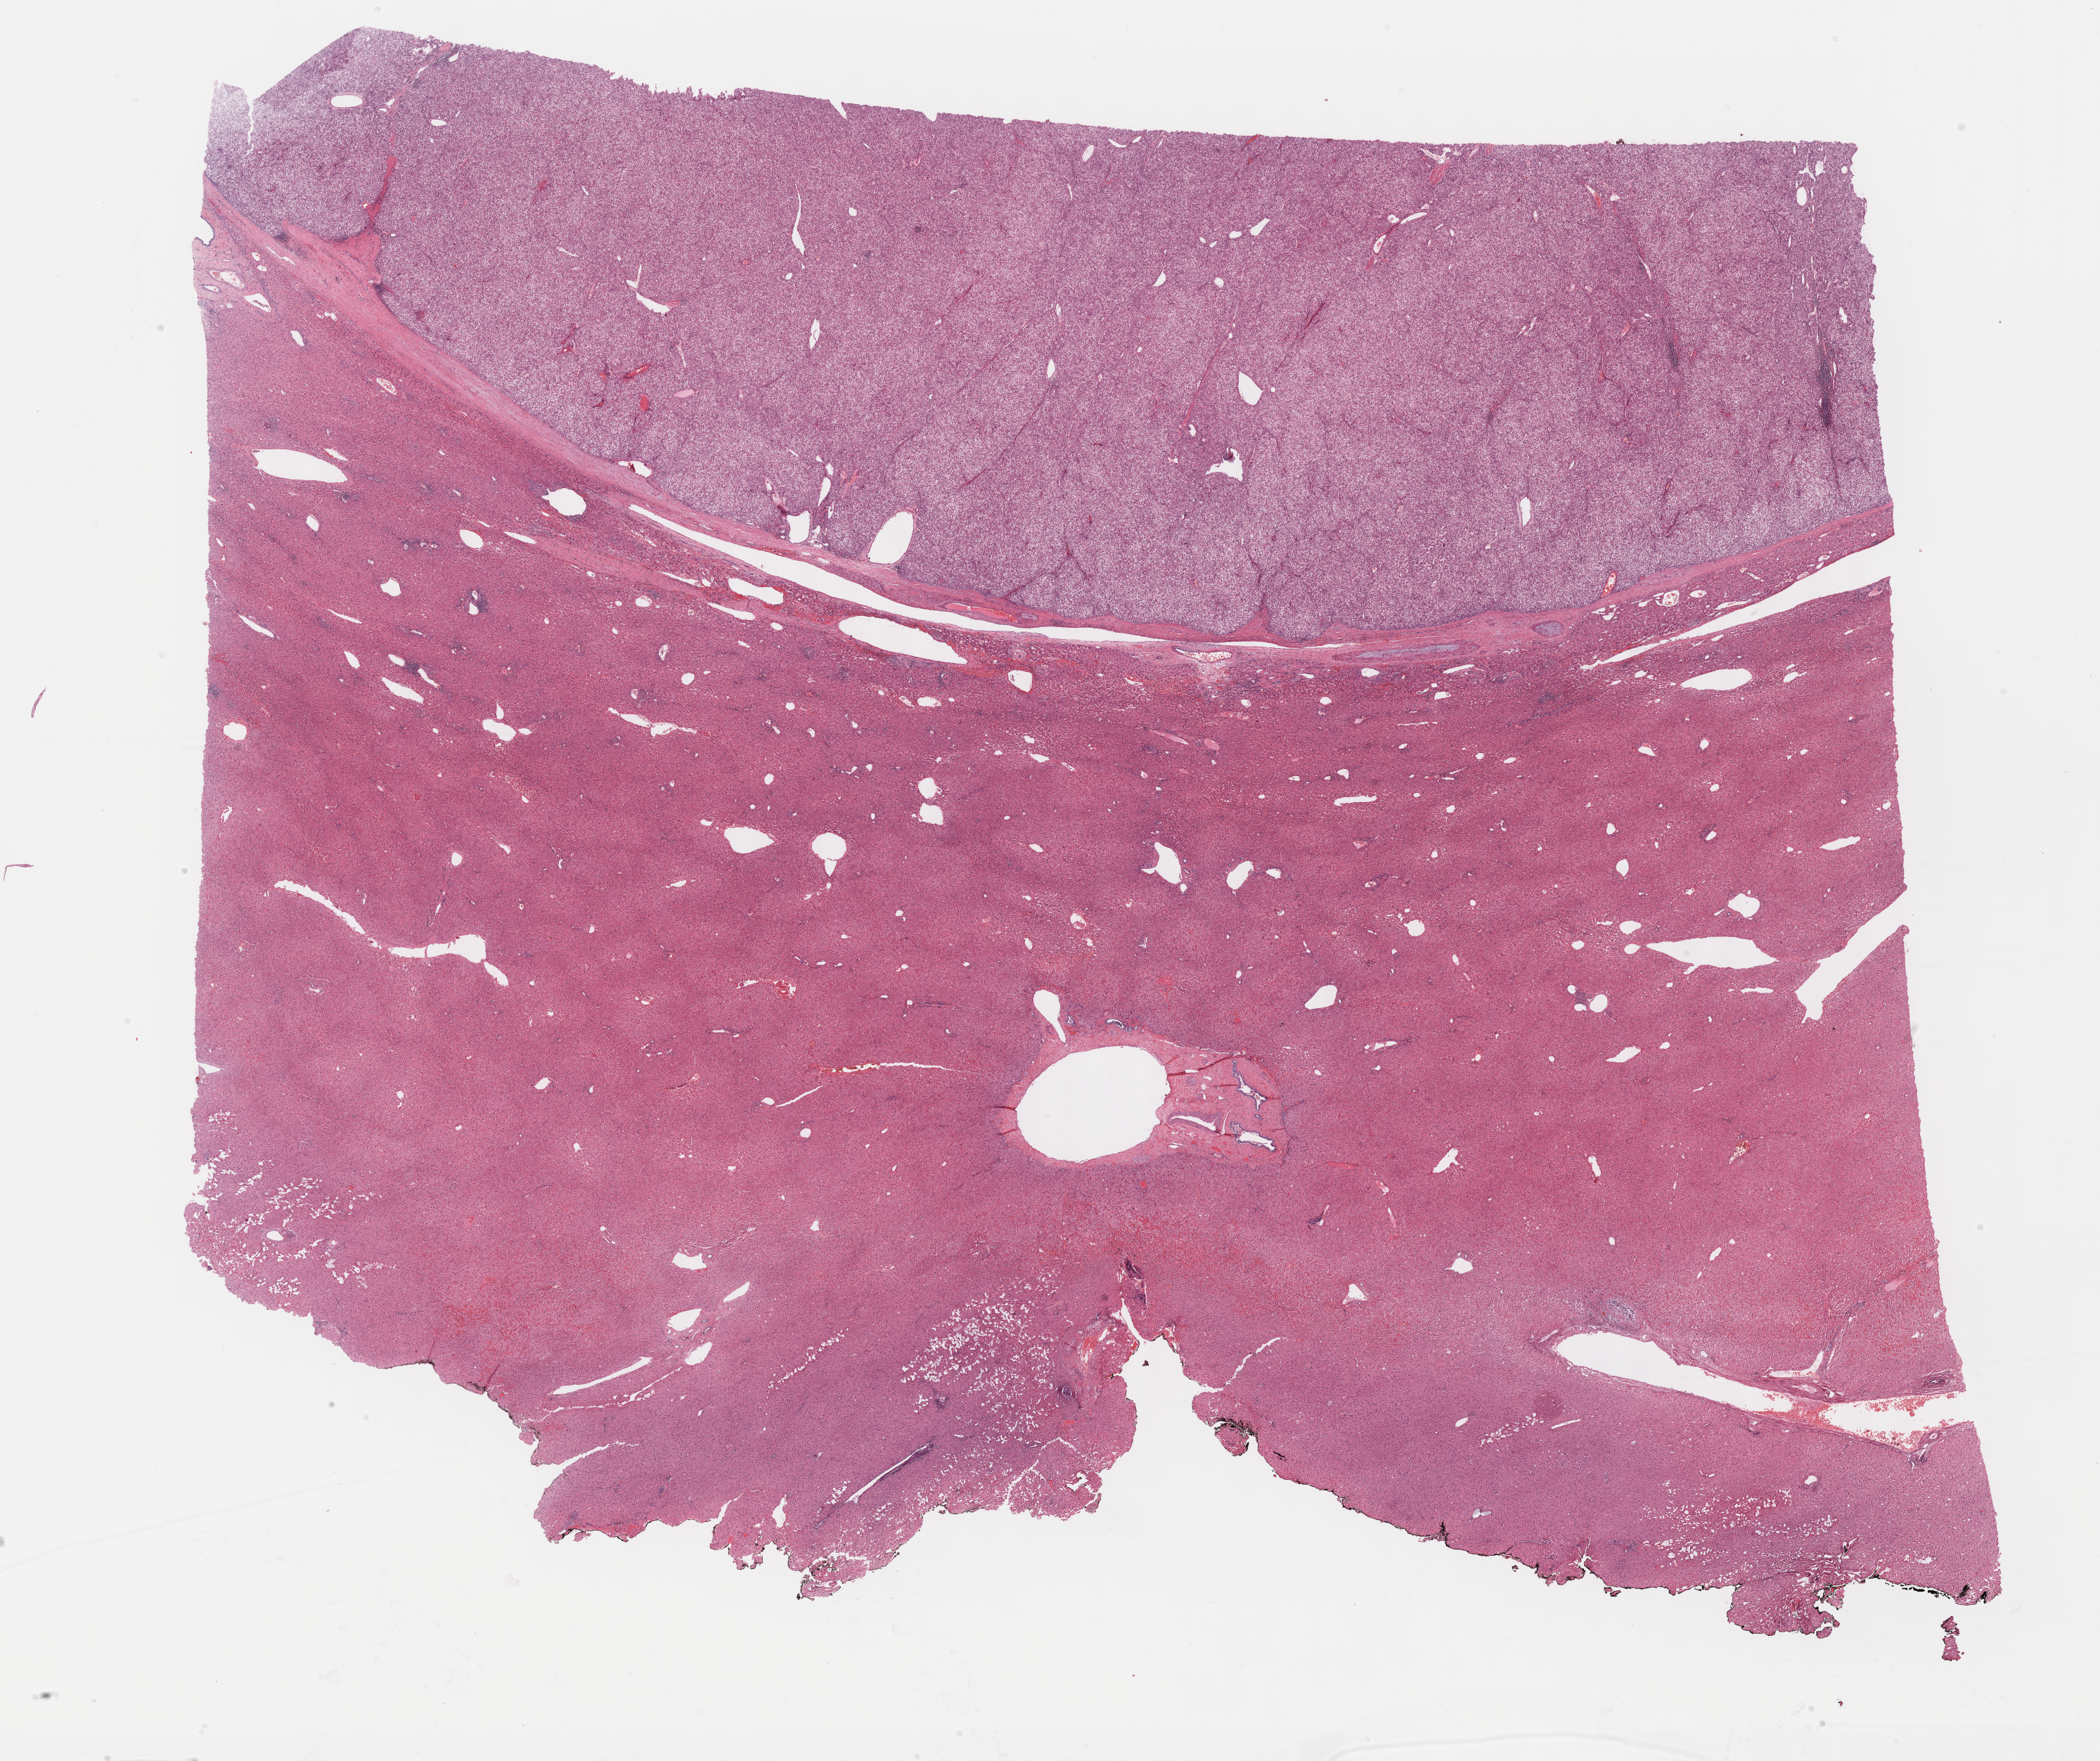
Whole-slide histology image, H&E, a low-resolution overview of the entire scanned area, about 24.2 x 20.3 mm; FFPE section; primary tumour sample from the liver. Male, age 58 years at initial diagnosis. Histologic grade: G2 (moderately differentiated).
Diagnosis: Hepatocellular carcinoma, NOS. AJCC pathologic stage: I.